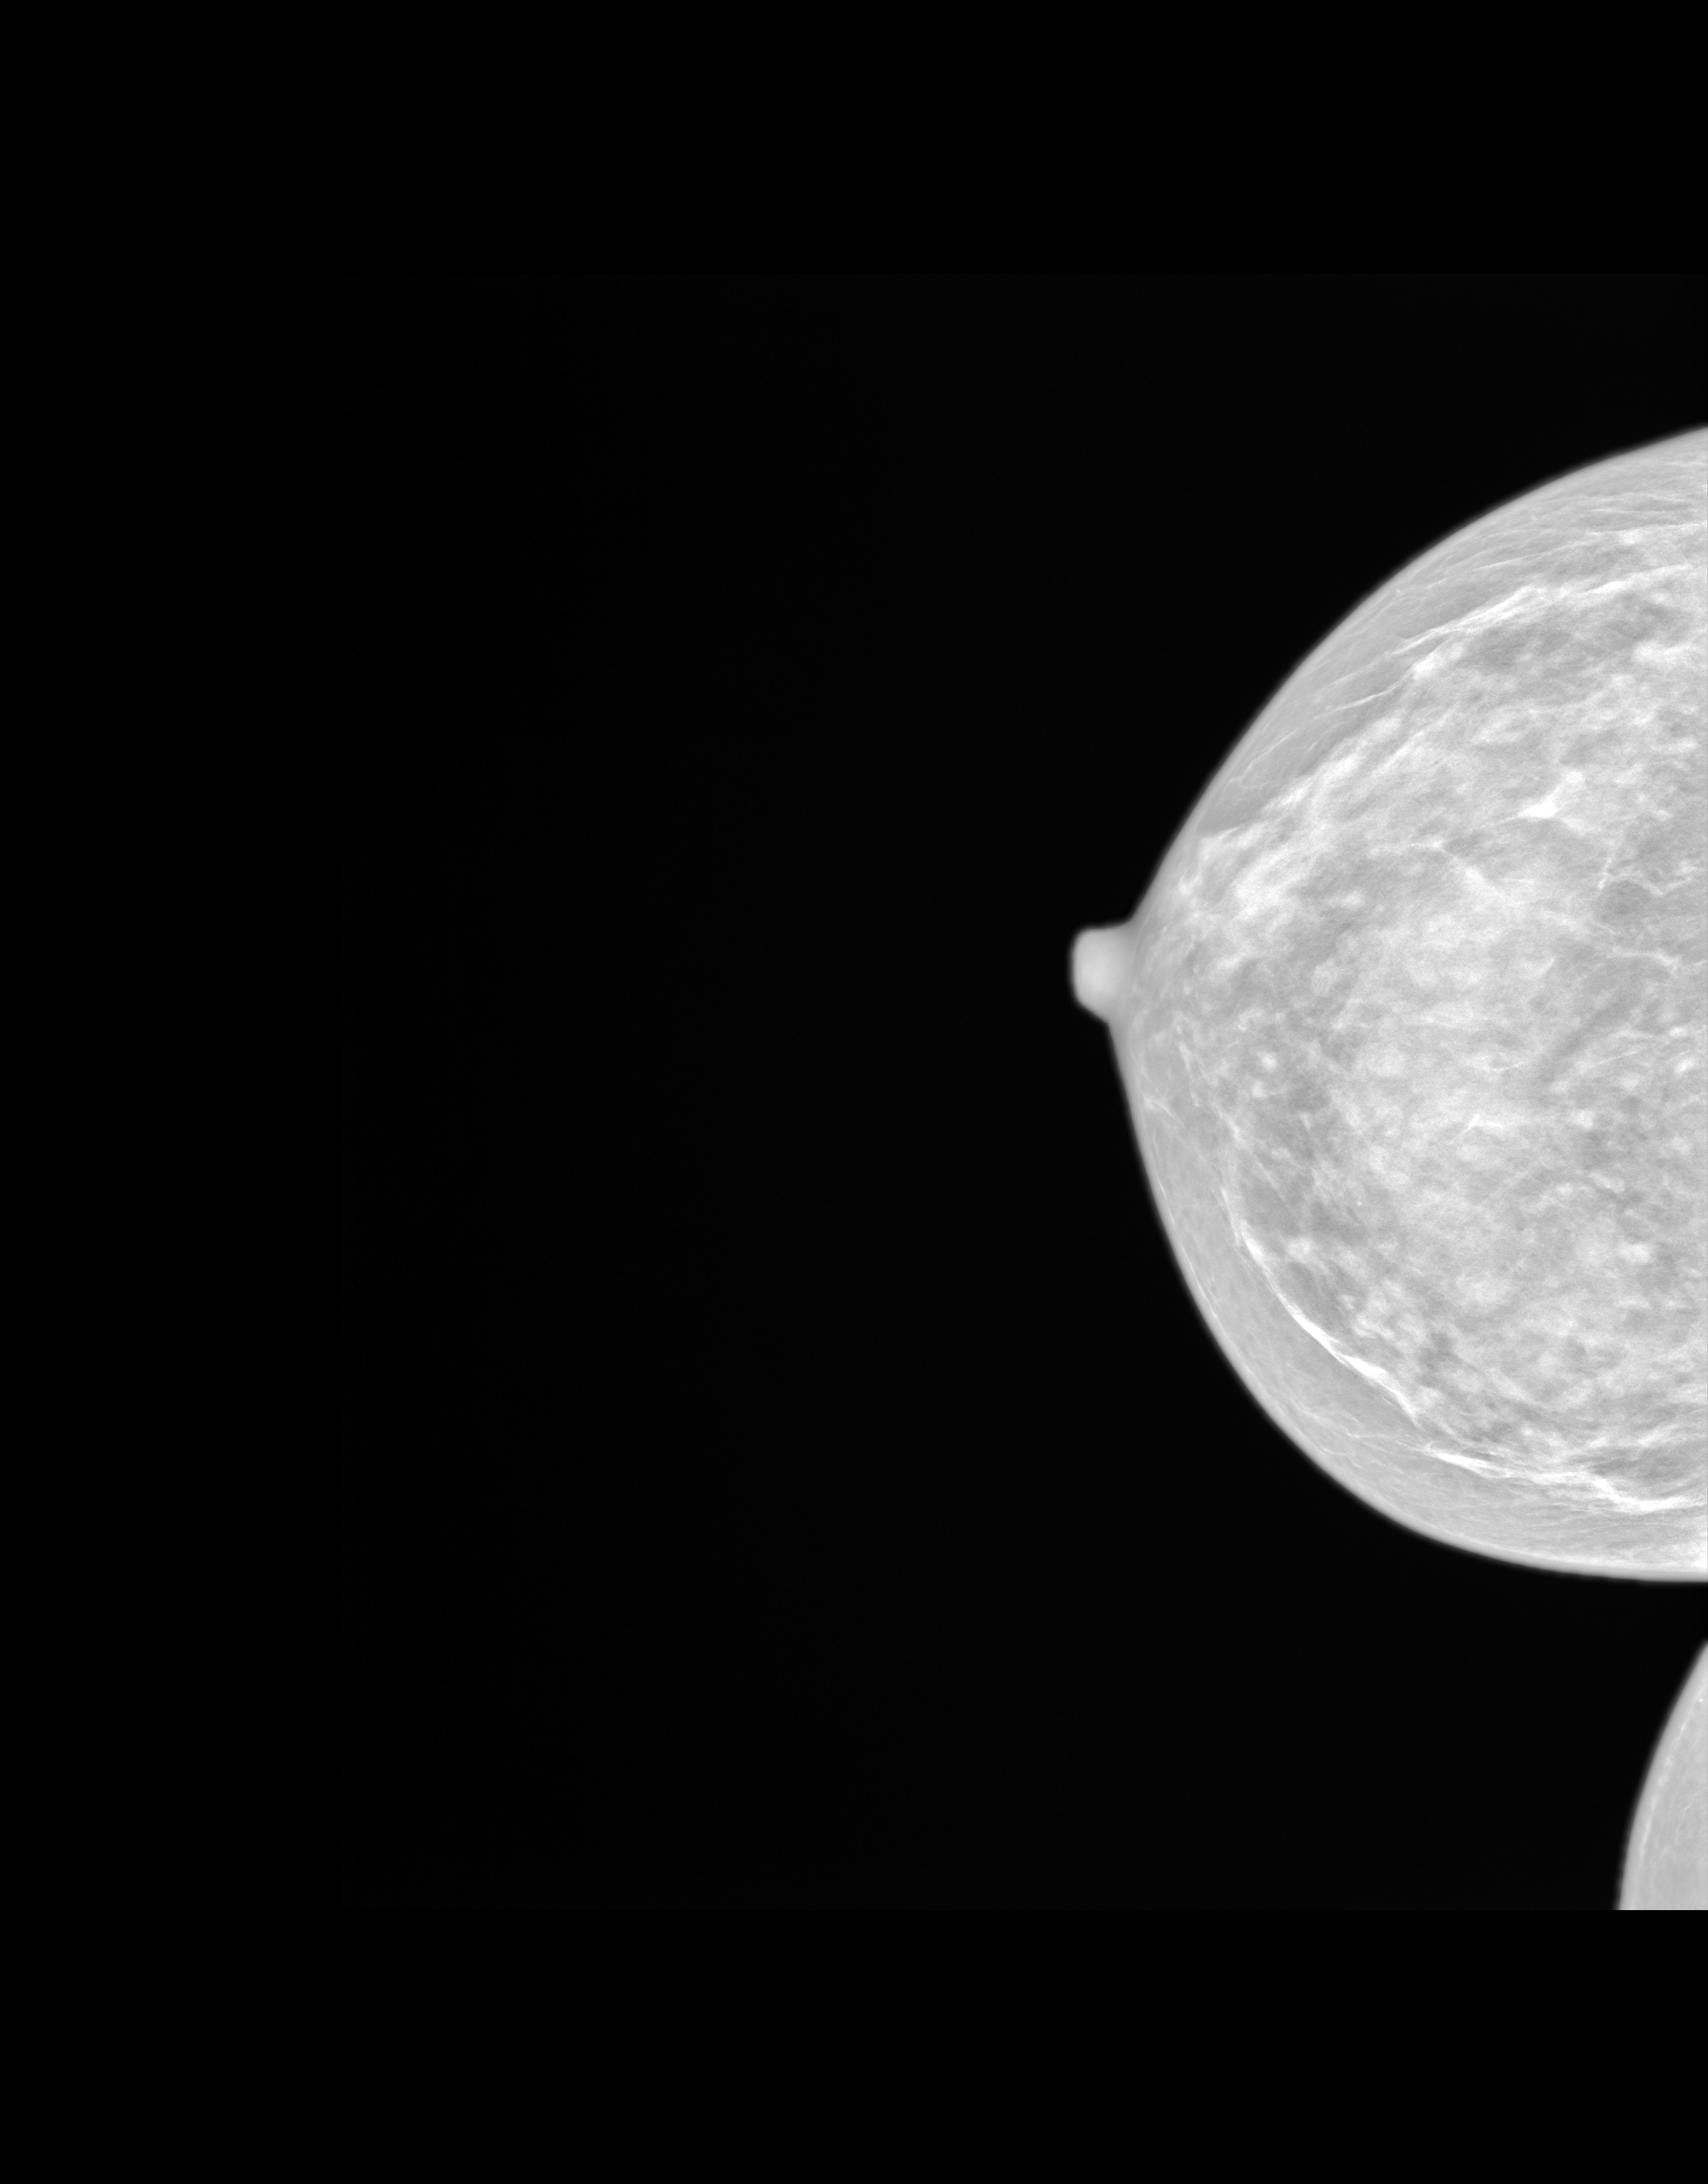
Synthesized 2-D mammogram reconstructed from digital breast tomosynthesis, right breast, cranio-caudal projection, screening examination. Female patient, age 60 years.
Breast density at the screening exam (both breasts): extremely dense (BI-RADS density category d). Final BI-RADS assessment for this screening round (tomosynthesis exam, both breasts): category 1. Recall: no recall after this screen.